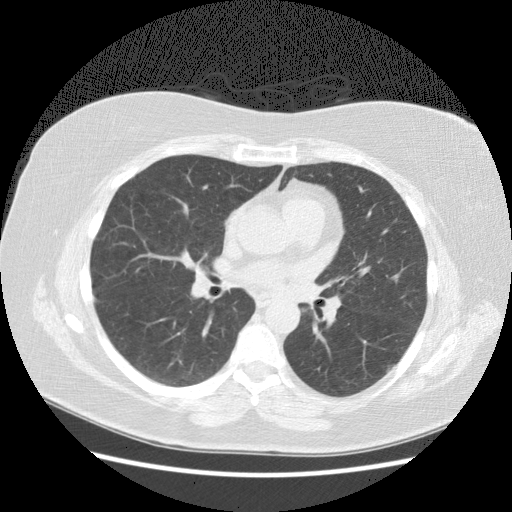
Low-dose screening chest CT, axial slice, baseline screening round, lung window (W 1500 / L -600 HU), slice 84 of 154 in the series, 512 × 512 image matrix, field of view 360 × 360 mm. Female, age 57 years at enrolment. Current smoker at enrolment.
Expert reader's lesion annotation, box from (x=373, y=347) to (x=408, y=383) px. No non-calcified nodule or mass ≥4 mm was recorded by the screening reader at this exam.